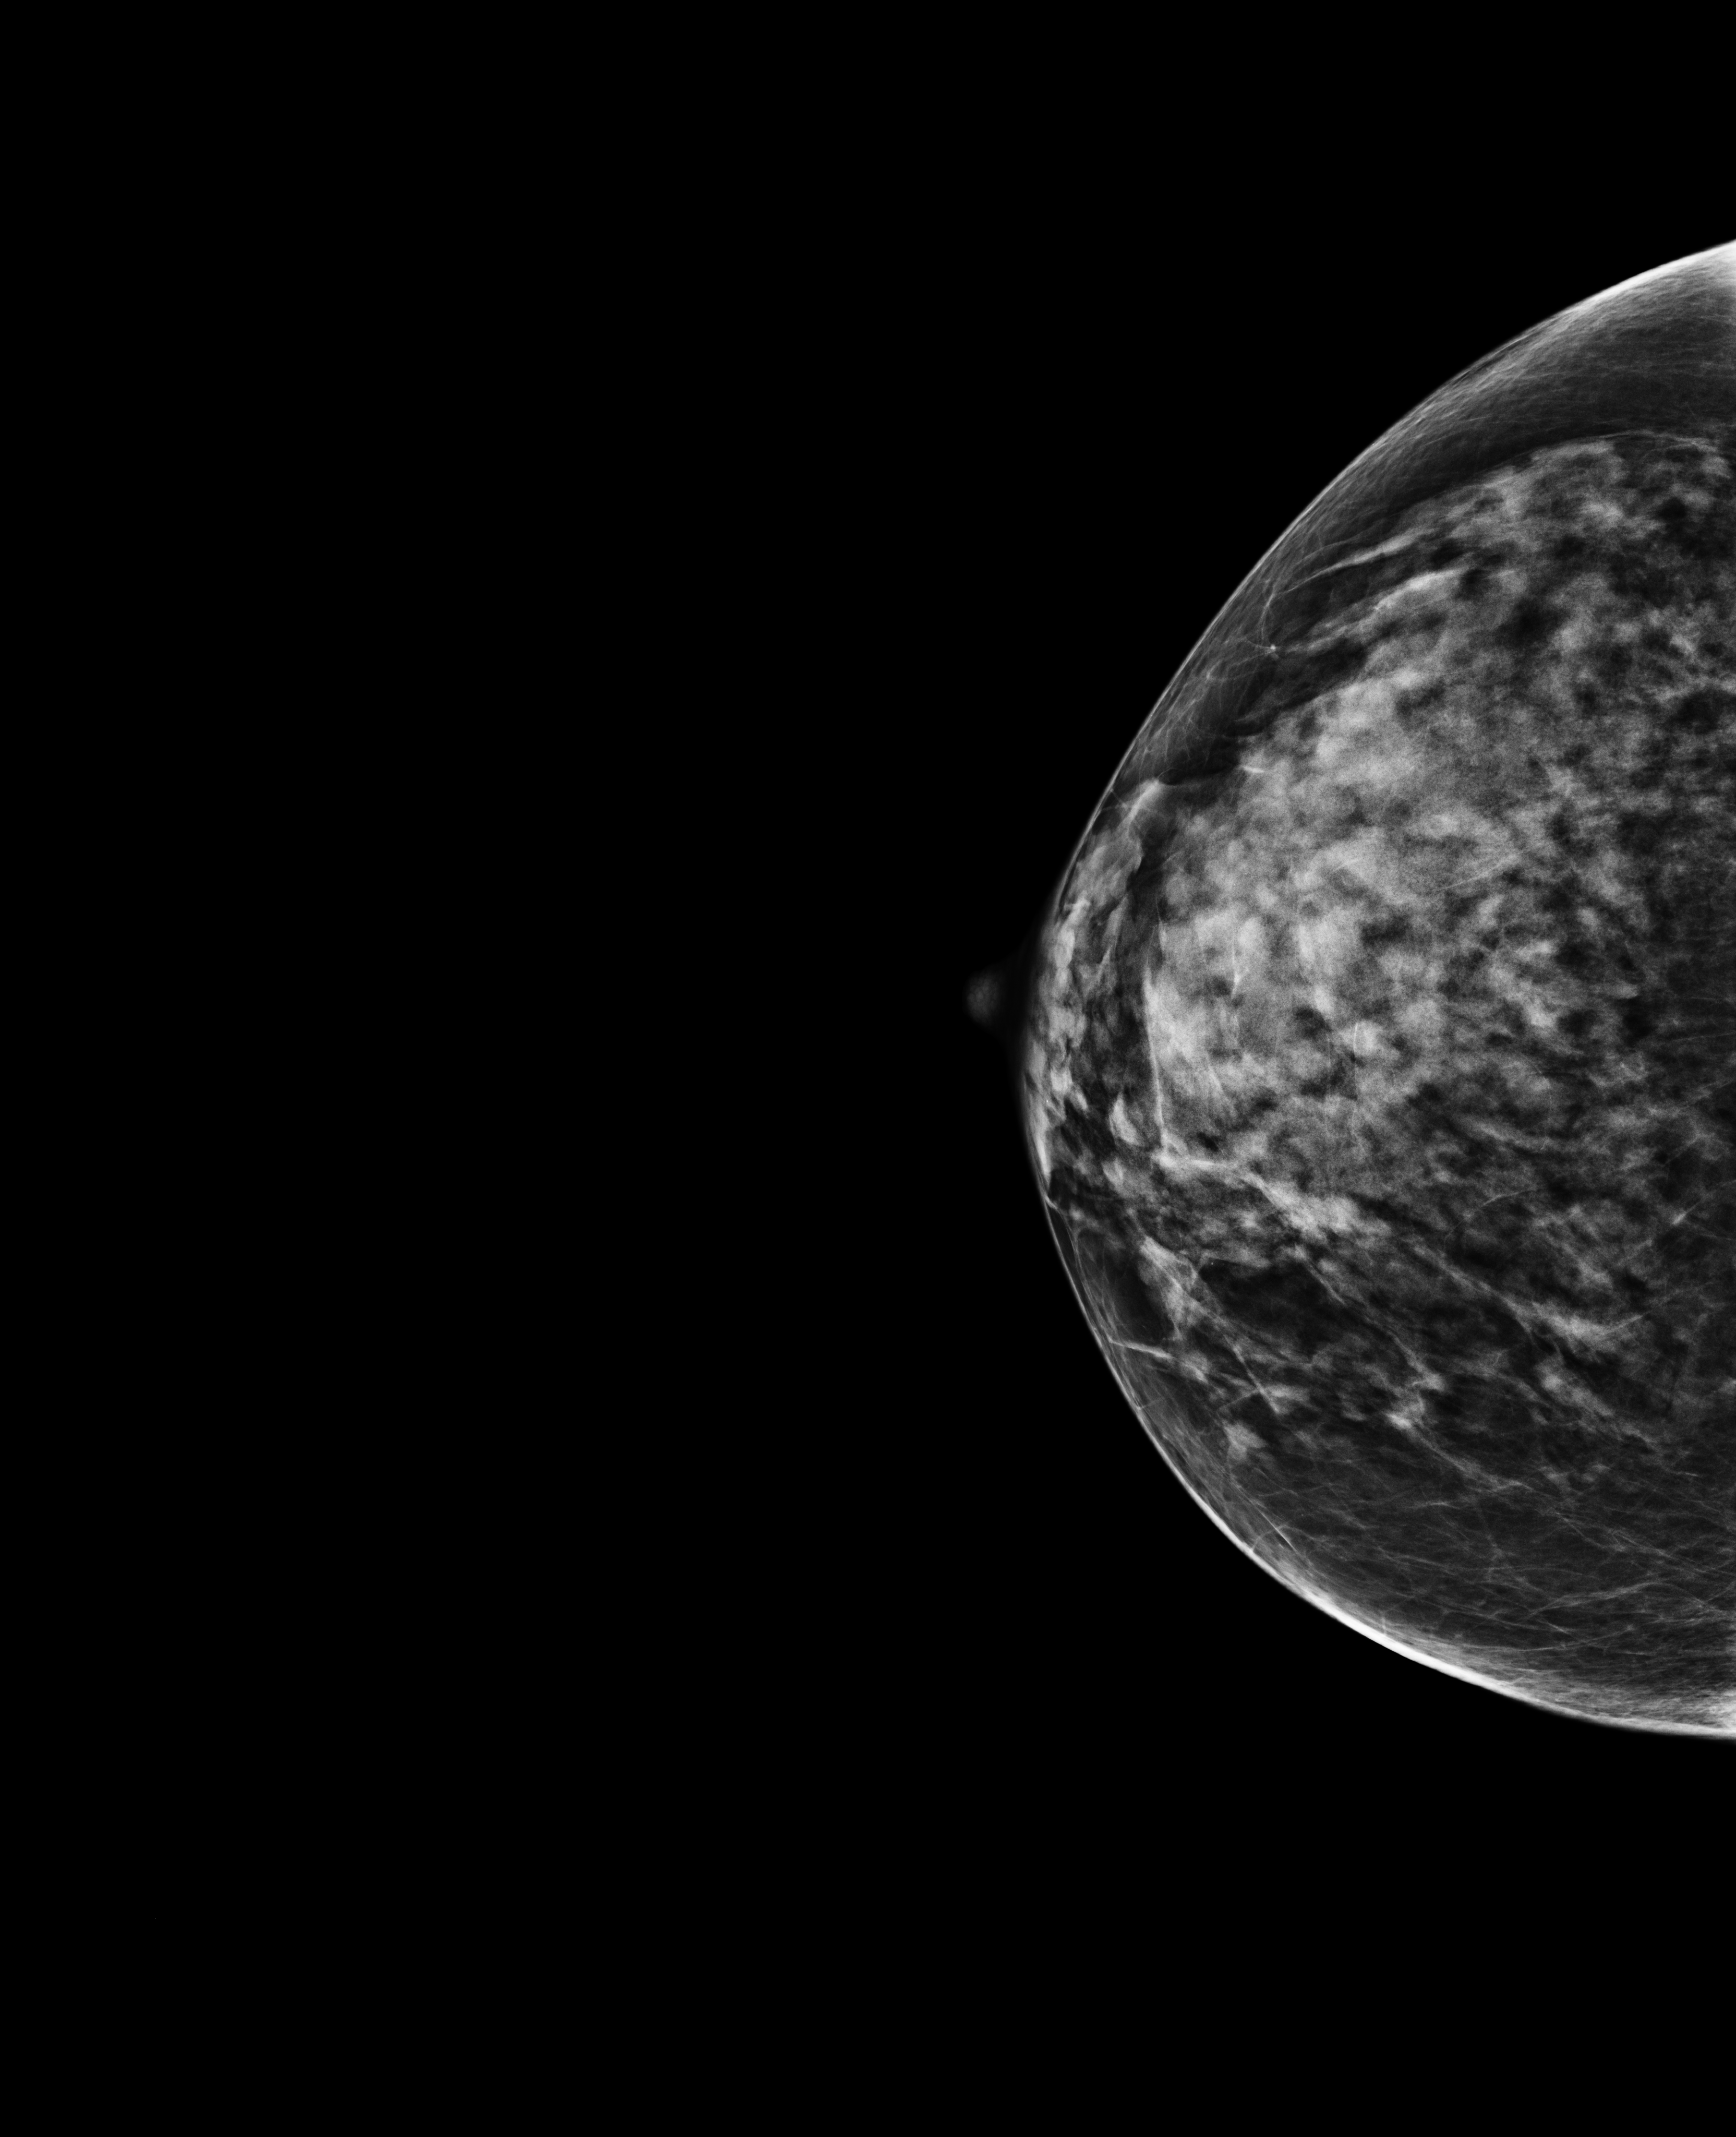
Digital mammogram (FFDM), right breast, cranio-caudal projection, annual screening mammography examination. Female patient, age 66 years.
BI-RADS breast density category at the screening exam (both breasts, scale 1–4): 3. Final BI-RADS category for the screening round (tomosynthesis exam, both breasts): category 1. Recall: no recall after this screen.